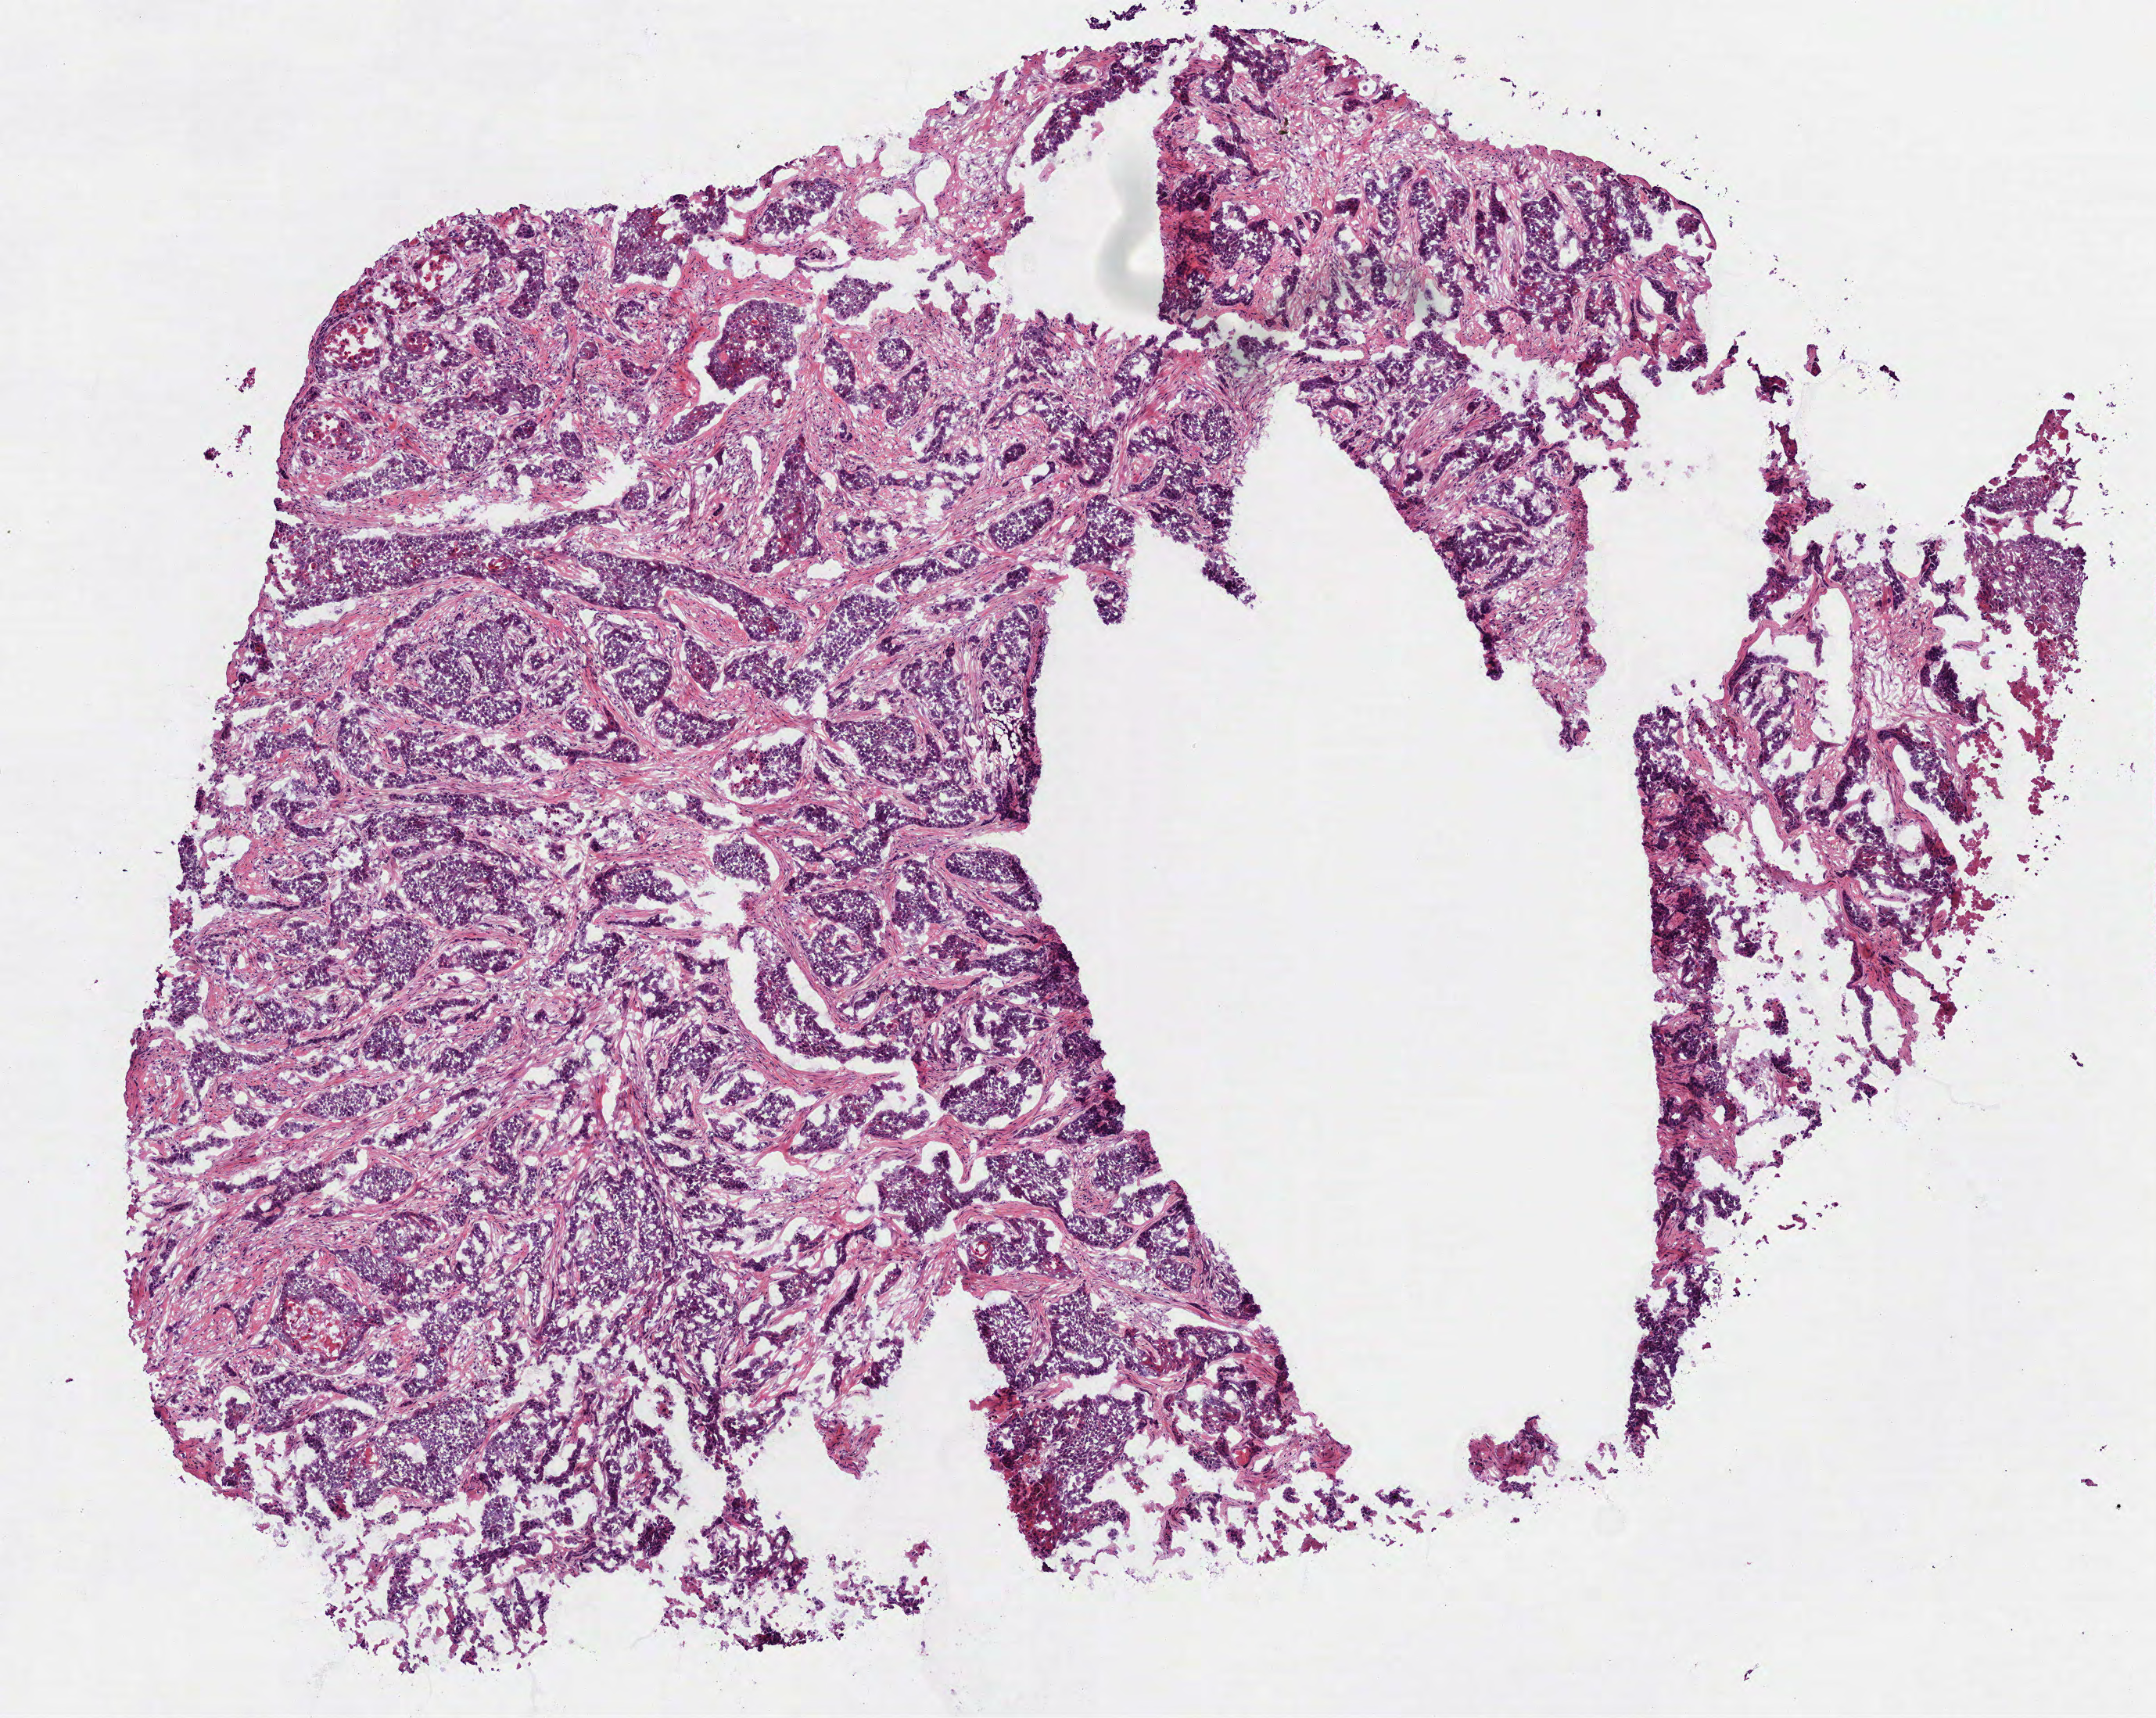
Digitized H&E tissue section (whole slide), low-resolution overview of the scanned area, about 5.6 x 4.4 mm (acquisition: 40x scan), frozen section from the bottom of the tissue portion, sample: primary tumour, head and neck. Female patient; age at initial diagnosis 79 years. Histologic grade: G2 (moderately differentiated). Slide review estimates, as recorded: tumour cells 99%, tumour nuclei 75%, normal cells 0%, stromal cells 0%, necrosis 1%. Inflammatory infiltration, as recorded: lymphocyte infiltration 10%, monocyte infiltration 0%, neutrophil infiltration 2%.
* lymph nodes positive (case pathology): 30 of 44 examined
* histologic diagnosis: Squamous cell carcinoma, NOS (floor of mouth, NOS)
* AJCC pathologic stage: IVB